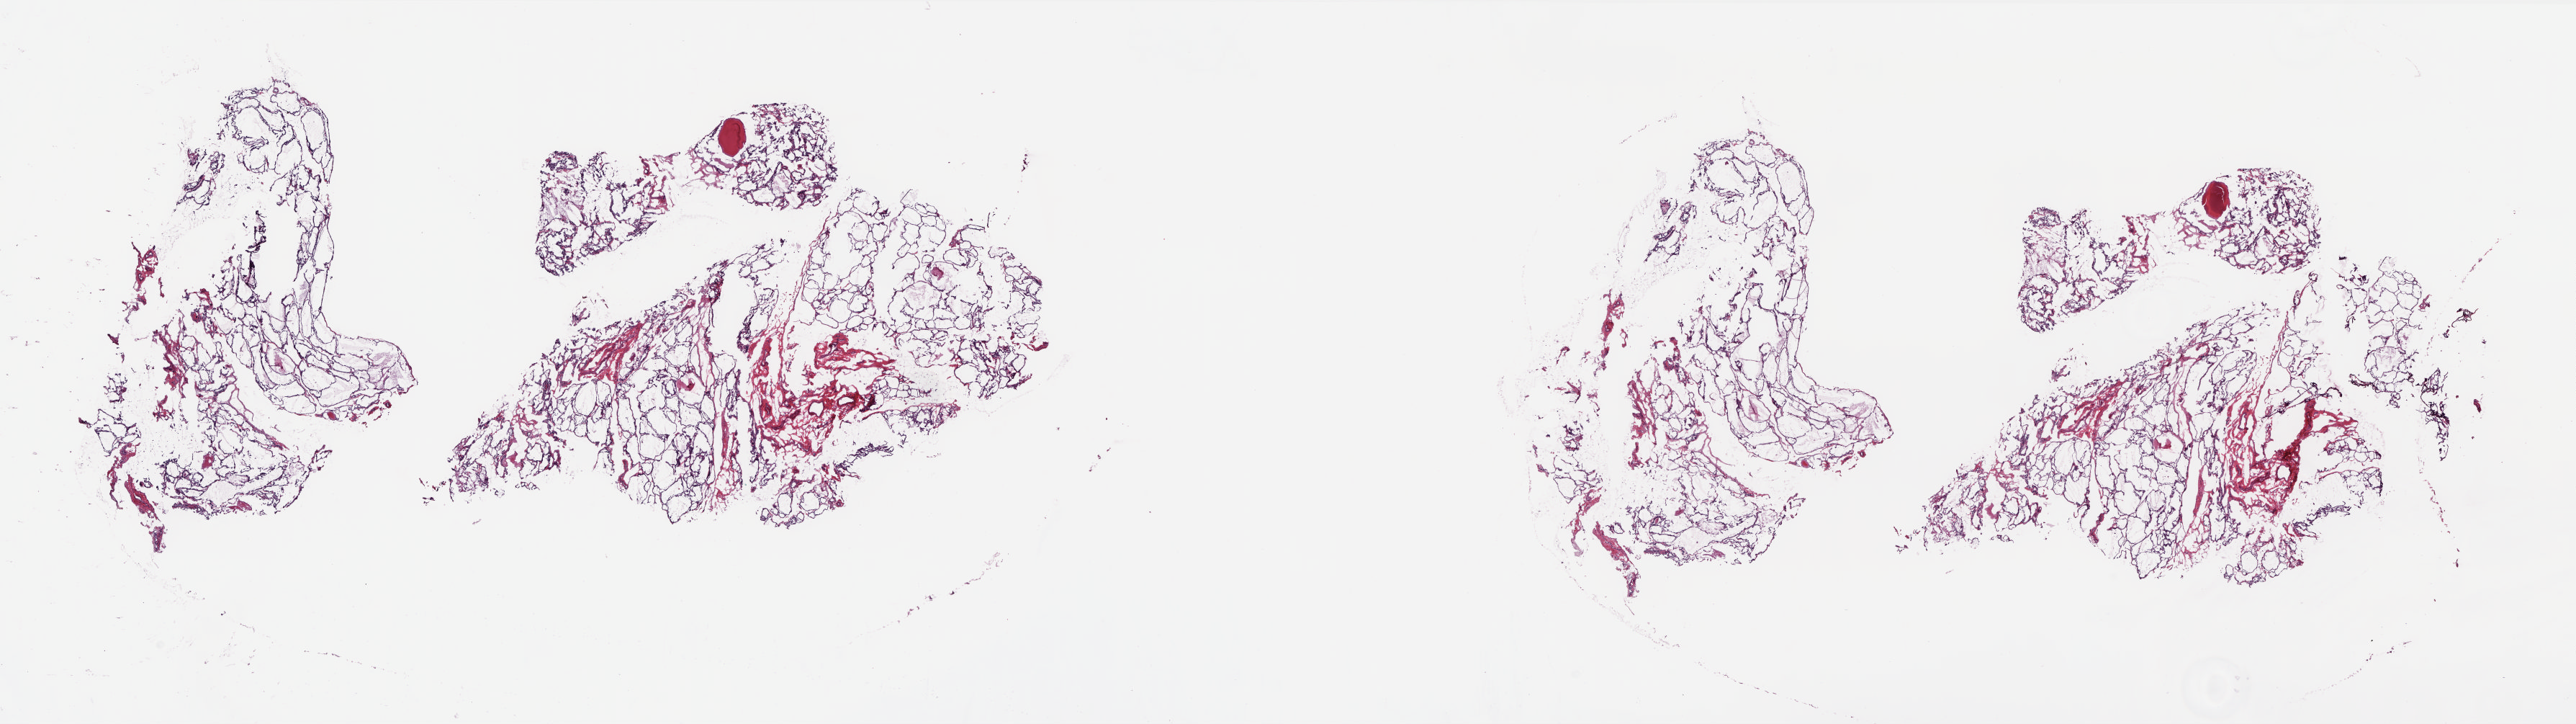
Whole-slide histology image, Hematoxylin and eosin (H&E) stained, whole scanned area (about 28.9 x 8.1 mm, from a 20x scan) shown as a low-resolution overview; frozen section from the top of the tissue portion; thyroid, solid tissue normal (non-tumour tissue) sample. Patient: female, age at initial diagnosis 41 years. Slide review estimates, as recorded: tumour cells 0%, tumour nuclei 0%, normal cells 100%, stromal cells 0%, necrosis 0%. Inflammatory infiltration, as recorded: lymphocyte infiltration 1%, monocyte infiltration 2%, neutrophil infiltration 0%.
• this section: solid tissue normal sample (biorepository sample class)
• patient diagnosis: Papillary adenocarcinoma, NOS (thyroid gland)